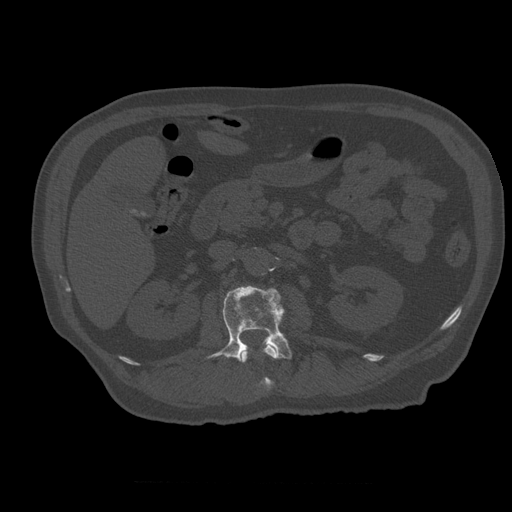
CT including the spine, one axial slice. Position 219 of 399 along the scan axis. 120 kVp. Bone window (W 1800 / L 400 HU). 512 × 512 image matrix, field of view 407 × 407 mm. Patient age 73 years. Case-level facts recorded for this patient, not image findings: primary cancer: prostate; vertebrae with lytic lesions (as recorded): L2.
Outlined on this slice (semi-automatically segmented with operator editing):
- L1 vertebra: bounding box <241,343,278,390> (left, top, right, bottom; pixels)
- L2 vertebra: <207,286,293,388>